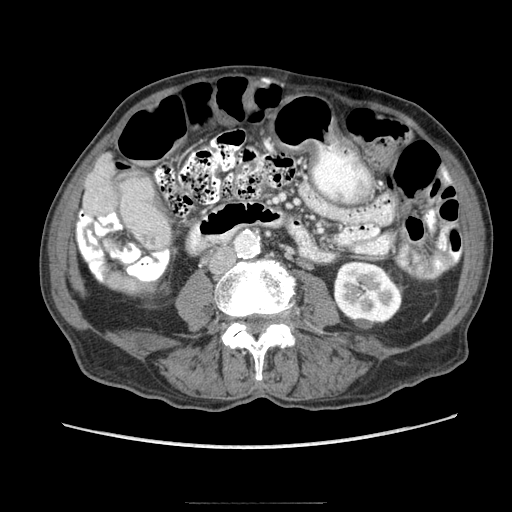
Contrast-enhanced abdominal CT (liver protocol), one axial slice. 140 kVp. Soft-tissue window (W 400 / L 40 HU). 2.5 mm slice thickness. 512 × 512 image matrix, field of view 360 × 360 mm. Case-level facts recorded for this patient, not image findings: diagnosis: hepatocellular carcinoma (patient treated with transarterial chemoembolisation; whether this scan precedes or follows treatment is not stated here); TNM stage (as recorded): Stage-I; Child-Pugh class: A; tumour nodularity: uninodular.
Structures marked on this image (semi-automatic segmentation, software-assisted and operator-edited):
- liver parenchyma outside the tumour (the mass and vessels are separate outlines, so this box may not span the whole liver): box from (x=82, y=152) to (x=118, y=216) px